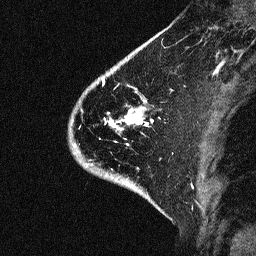
Breast MRI (dynamic contrast-enhanced), one sagittal slice; position 15 of 64 along the scan axis; dynamic contrast-enhanced study with each time point stored as its own series, time point 2 of 3 at this slice position (early post-contrast, ordered by acquisition time); 1.5 T; TE 4.5 ms, TR 11 ms; 2.06 mm slice thickness; 256 × 256 image matrix, field of view 200 × 200 mm. Patient: female, 46 years. From the clinical record (not read from this slice): setting: breast cancer imaged before/during neoadjuvant chemotherapy; receptor status: HER2-positive.
Structures marked on this image (semi-automatically segmented with operator editing):
- analysis volume of interest (the breast-tissue region the enhancement analysis was run in; not a lesion): bounding box [x1, y1, x2, y2] px = [43, 72, 176, 177]
- tumour enhancement mask (voxels above the 90 % enhancement threshold inside the analysis volume of interest): [100, 83, 148, 139]